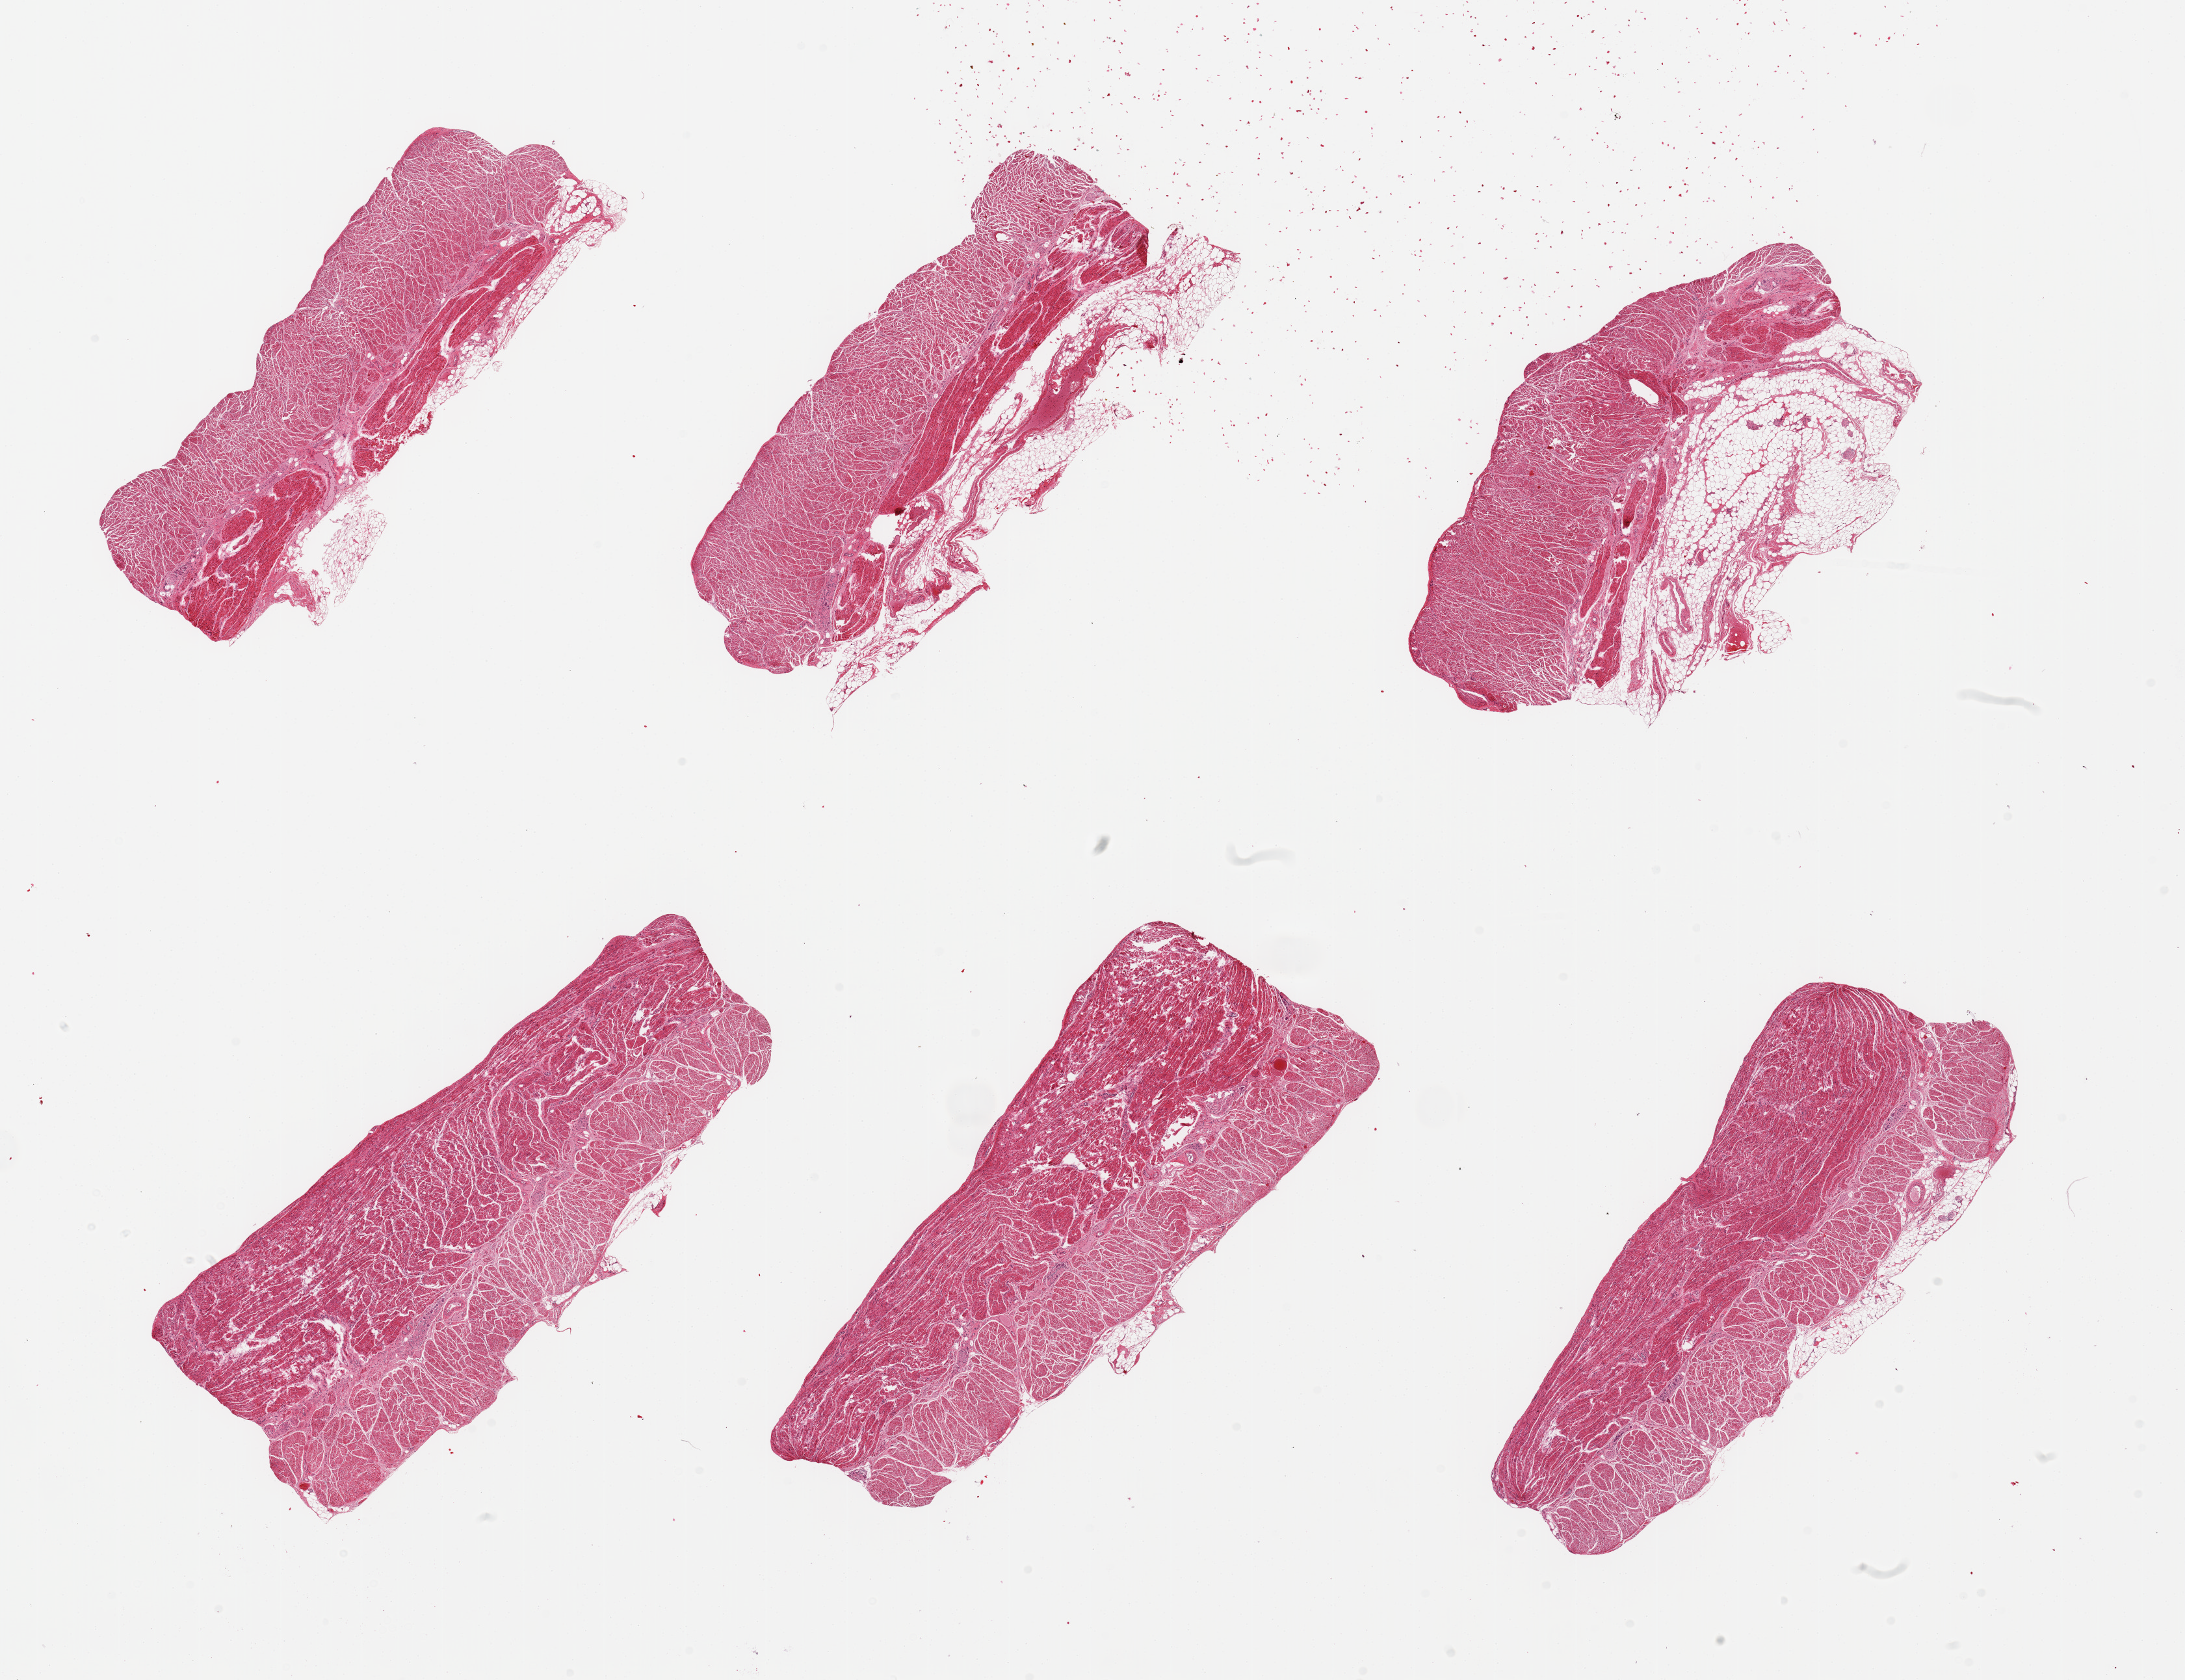
Digitized H&E-stained section — a low-resolution overview of the entire scanned area, about 26.6 x 20.4 mm. PAXgene-fixed paraffin-embedded (PFPE) section. Target tissue: gastroesophageal junction. Donor tissue sample. Male donor.
Reviewer comment on this tissue sample: 6 pieces; smooth muscle layers with adherent external fat from 10% up to 40% on 3 pieces.